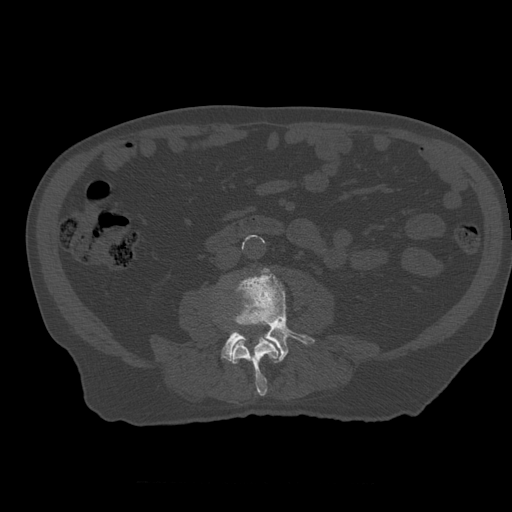
CT including the spine, one axial slice; position 176 of 399 along the scan axis; 120 kVp; bone window (W 1800 / L 400 HU); 512 × 512 image matrix, field of view 407 × 407 mm. Patient age 73 years. Case-level facts recorded for this patient, not image findings: primary cancer: prostate.
Annotated regions visible in this slice (semi-automatically segmented with operator editing):
- L3 vertebra: bounding box <231,315,283,396> (left, top, right, bottom; pixels)
- L4 vertebra: <221,268,315,363>